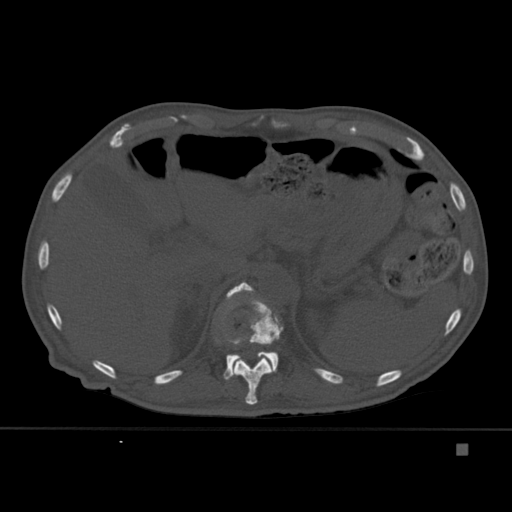
CT including the spine, one axial slice; position 211 of 451 along the scan axis; bone window (W 1800 / L 400 HU); 512 × 512 image matrix, field of view 378 × 378 mm. Male patient, age 75 years. From the clinical record (not read from this slice): primary cancer: prostate.
Structures marked on this image (semi-automatically segmented with operator editing):
- T11 vertebra: bounding box <230,298,283,405> (left, top, right, bottom; pixels)
- T12 vertebra: <217,281,283,380>